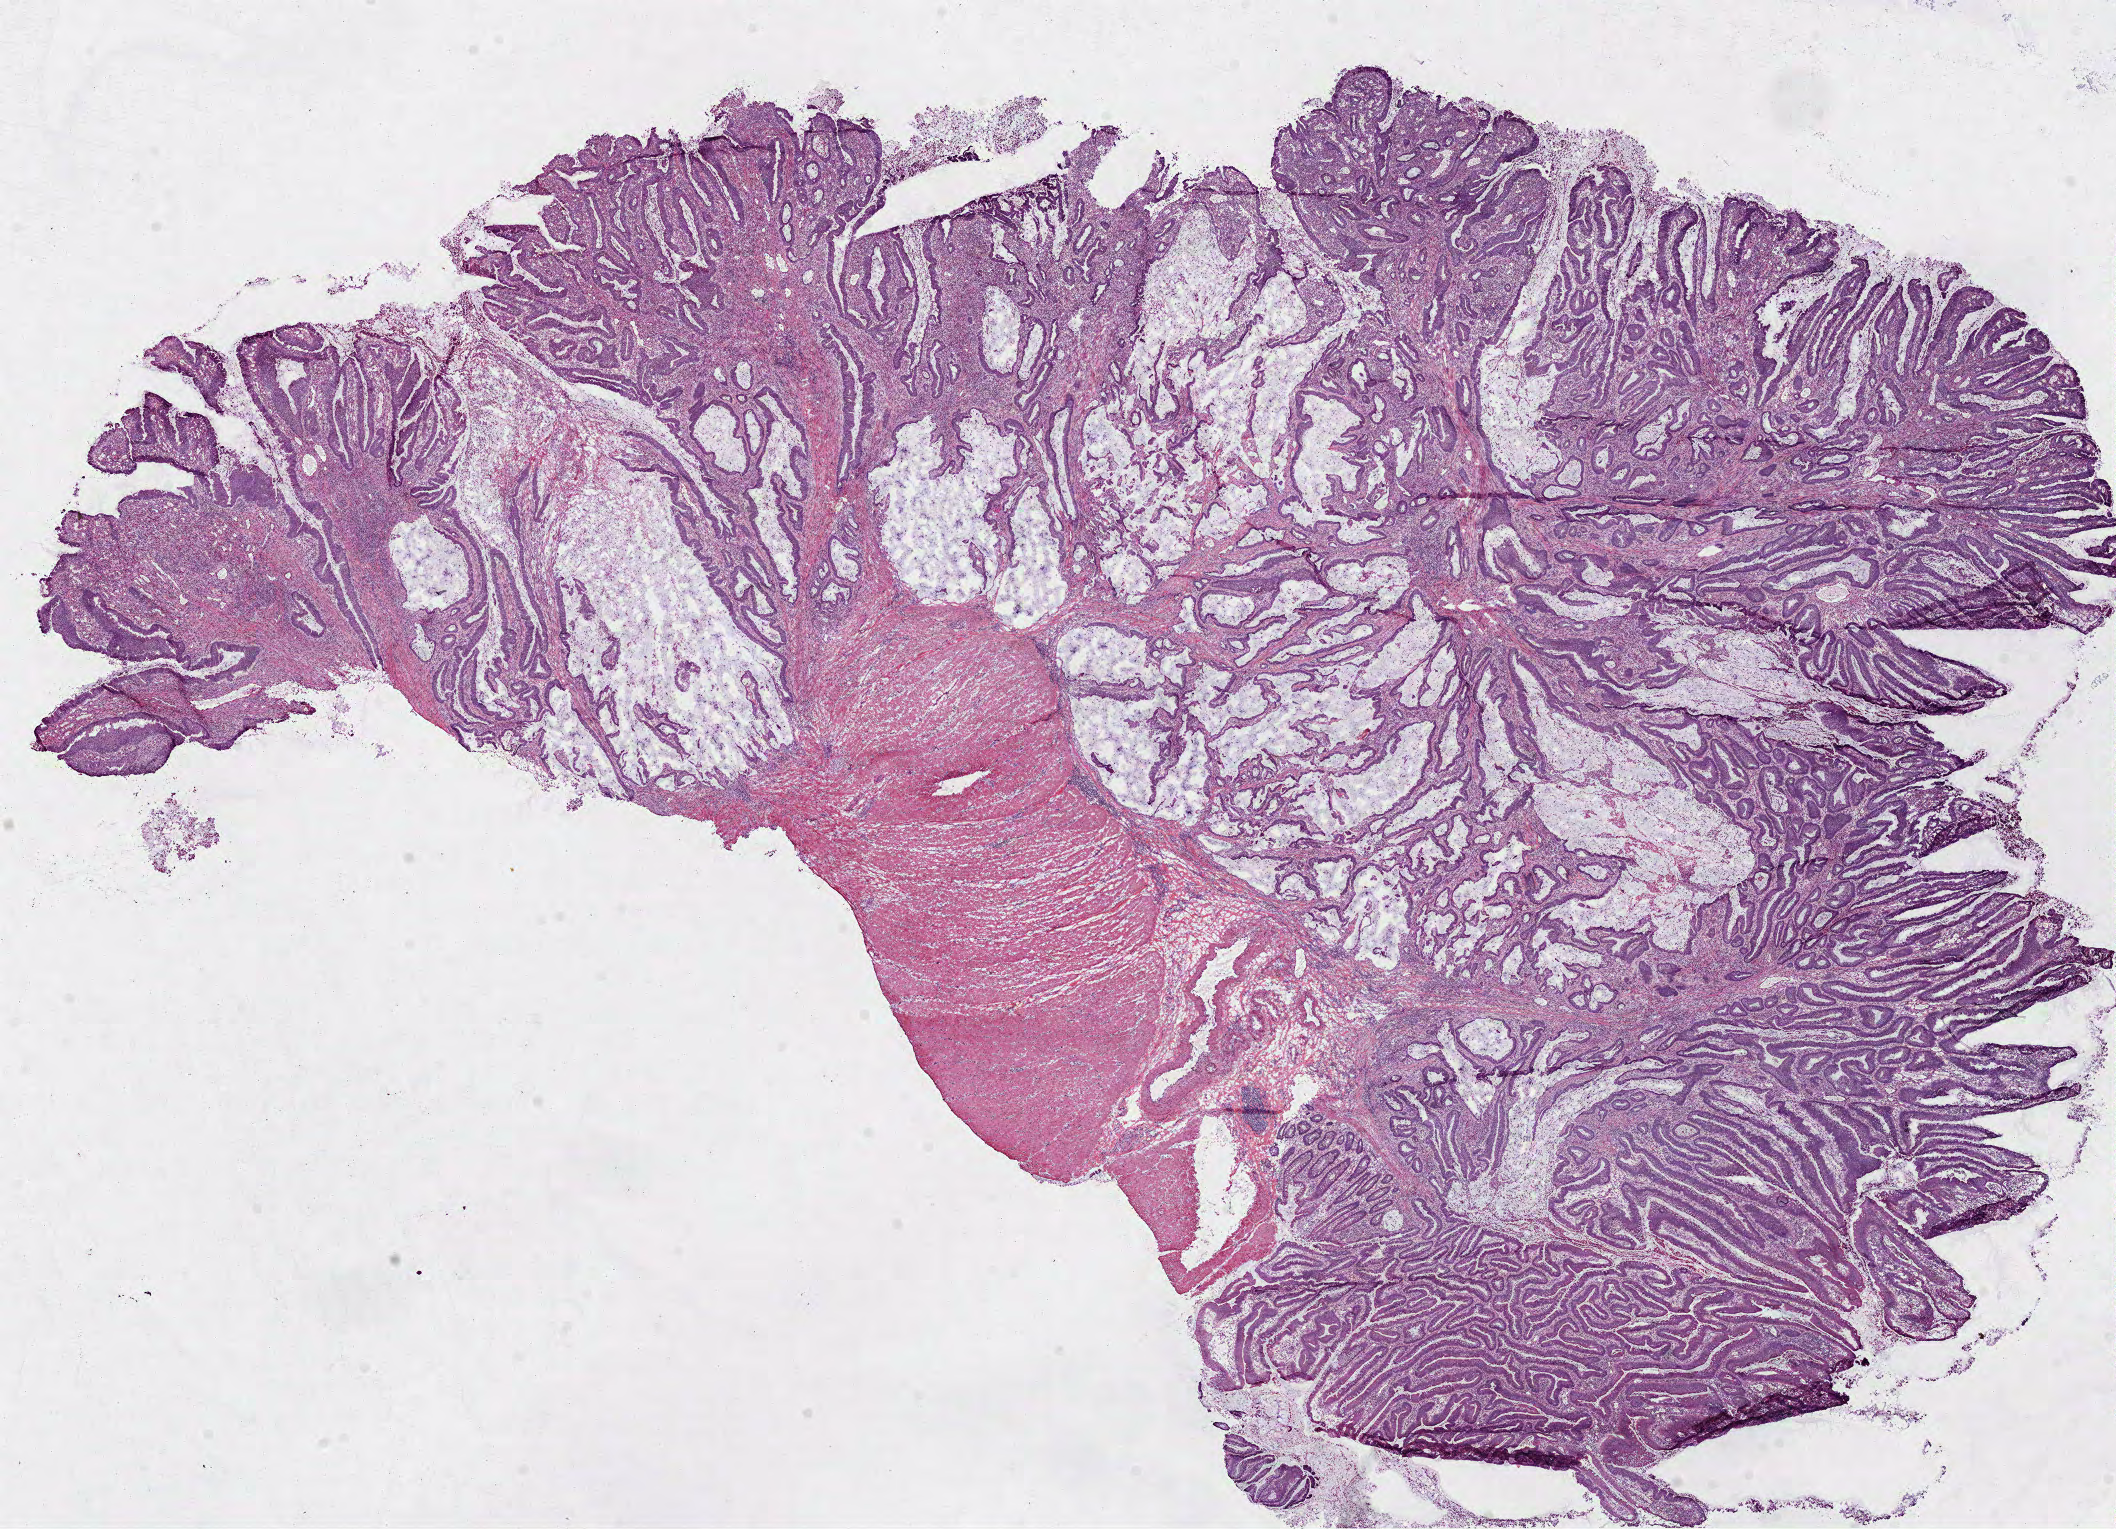
H&E-stained whole-slide image — a low-resolution overview of the entire scanned area, about 17.1 x 12.3 mm (slide scanned at 40x), frozen section from the bottom of the tissue portion, sample: primary tumour, colon. Patient: male, age at initial diagnosis 39 years. Composition of this section per pathologist review: tumour cells 63%, tumour nuclei 80%, normal cells 12%, stromal cells 15%, necrosis 10%.
• AJCC pathologic stage: IIA
• pathologic diagnosis: Adenocarcinoma, NOS (hepatic flexure of colon)
• TNM: T3 N0 M0